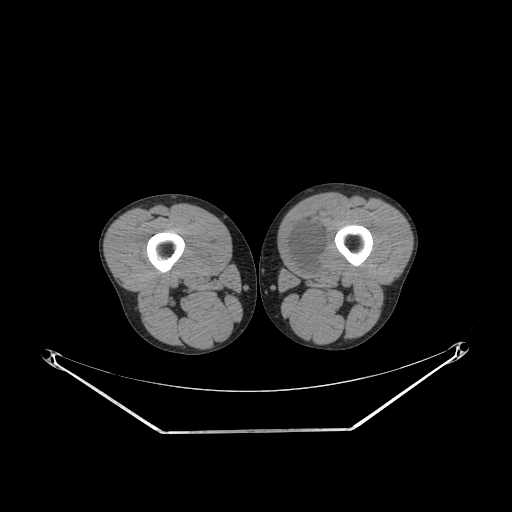
CT of an extremity soft-tissue mass (from a PET/CT study), one axial slice; slice 234 of 311 in the series (ordered by position); reconstruction kernel SOFT; 140 kVp; soft-tissue window (W 400 / L 40 HU); 3.75 mm slice thickness; 512 × 512 image matrix. Male patient. Case-level facts recorded for this patient, not image findings: histological type: mixoid liposarcoma; grade: low; site of the primary tumour: left thigh.
Outlined on this slice (expert contour drawn on MRI and transferred to this co-registered scan by the dataset authors):
- gross tumour volume (mass): bounding box [x1, y1, x2, y2] px = [285, 219, 328, 277]